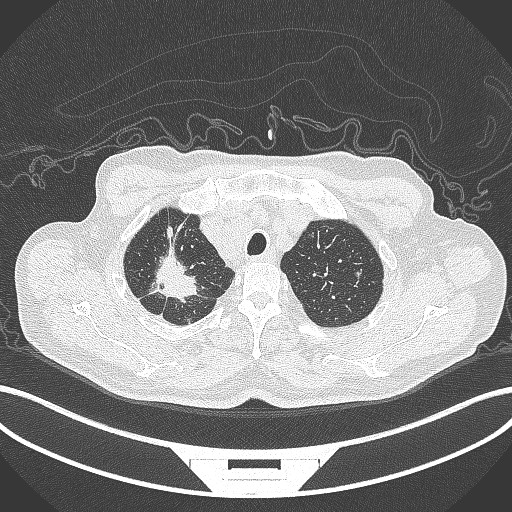
Chest CT, one axial slice; slice 333 of 407 in the series (ordered by position); 120 kVp; lung window (W 1500 / L -600 HU); 1 mm slice thickness; 512 × 512 image matrix, field of view 400 × 400 mm. Male patient, age 69 years. From the clinical record (not read from this slice): clinical TNM (as recorded): T1c N1 M1.
Structures marked on this image (bounding box drawn by a radiologist):
- lung tumour (recorded histology: adenocarcinoma): bounding box [x1, y1, x2, y2] px = [141, 246, 211, 303]